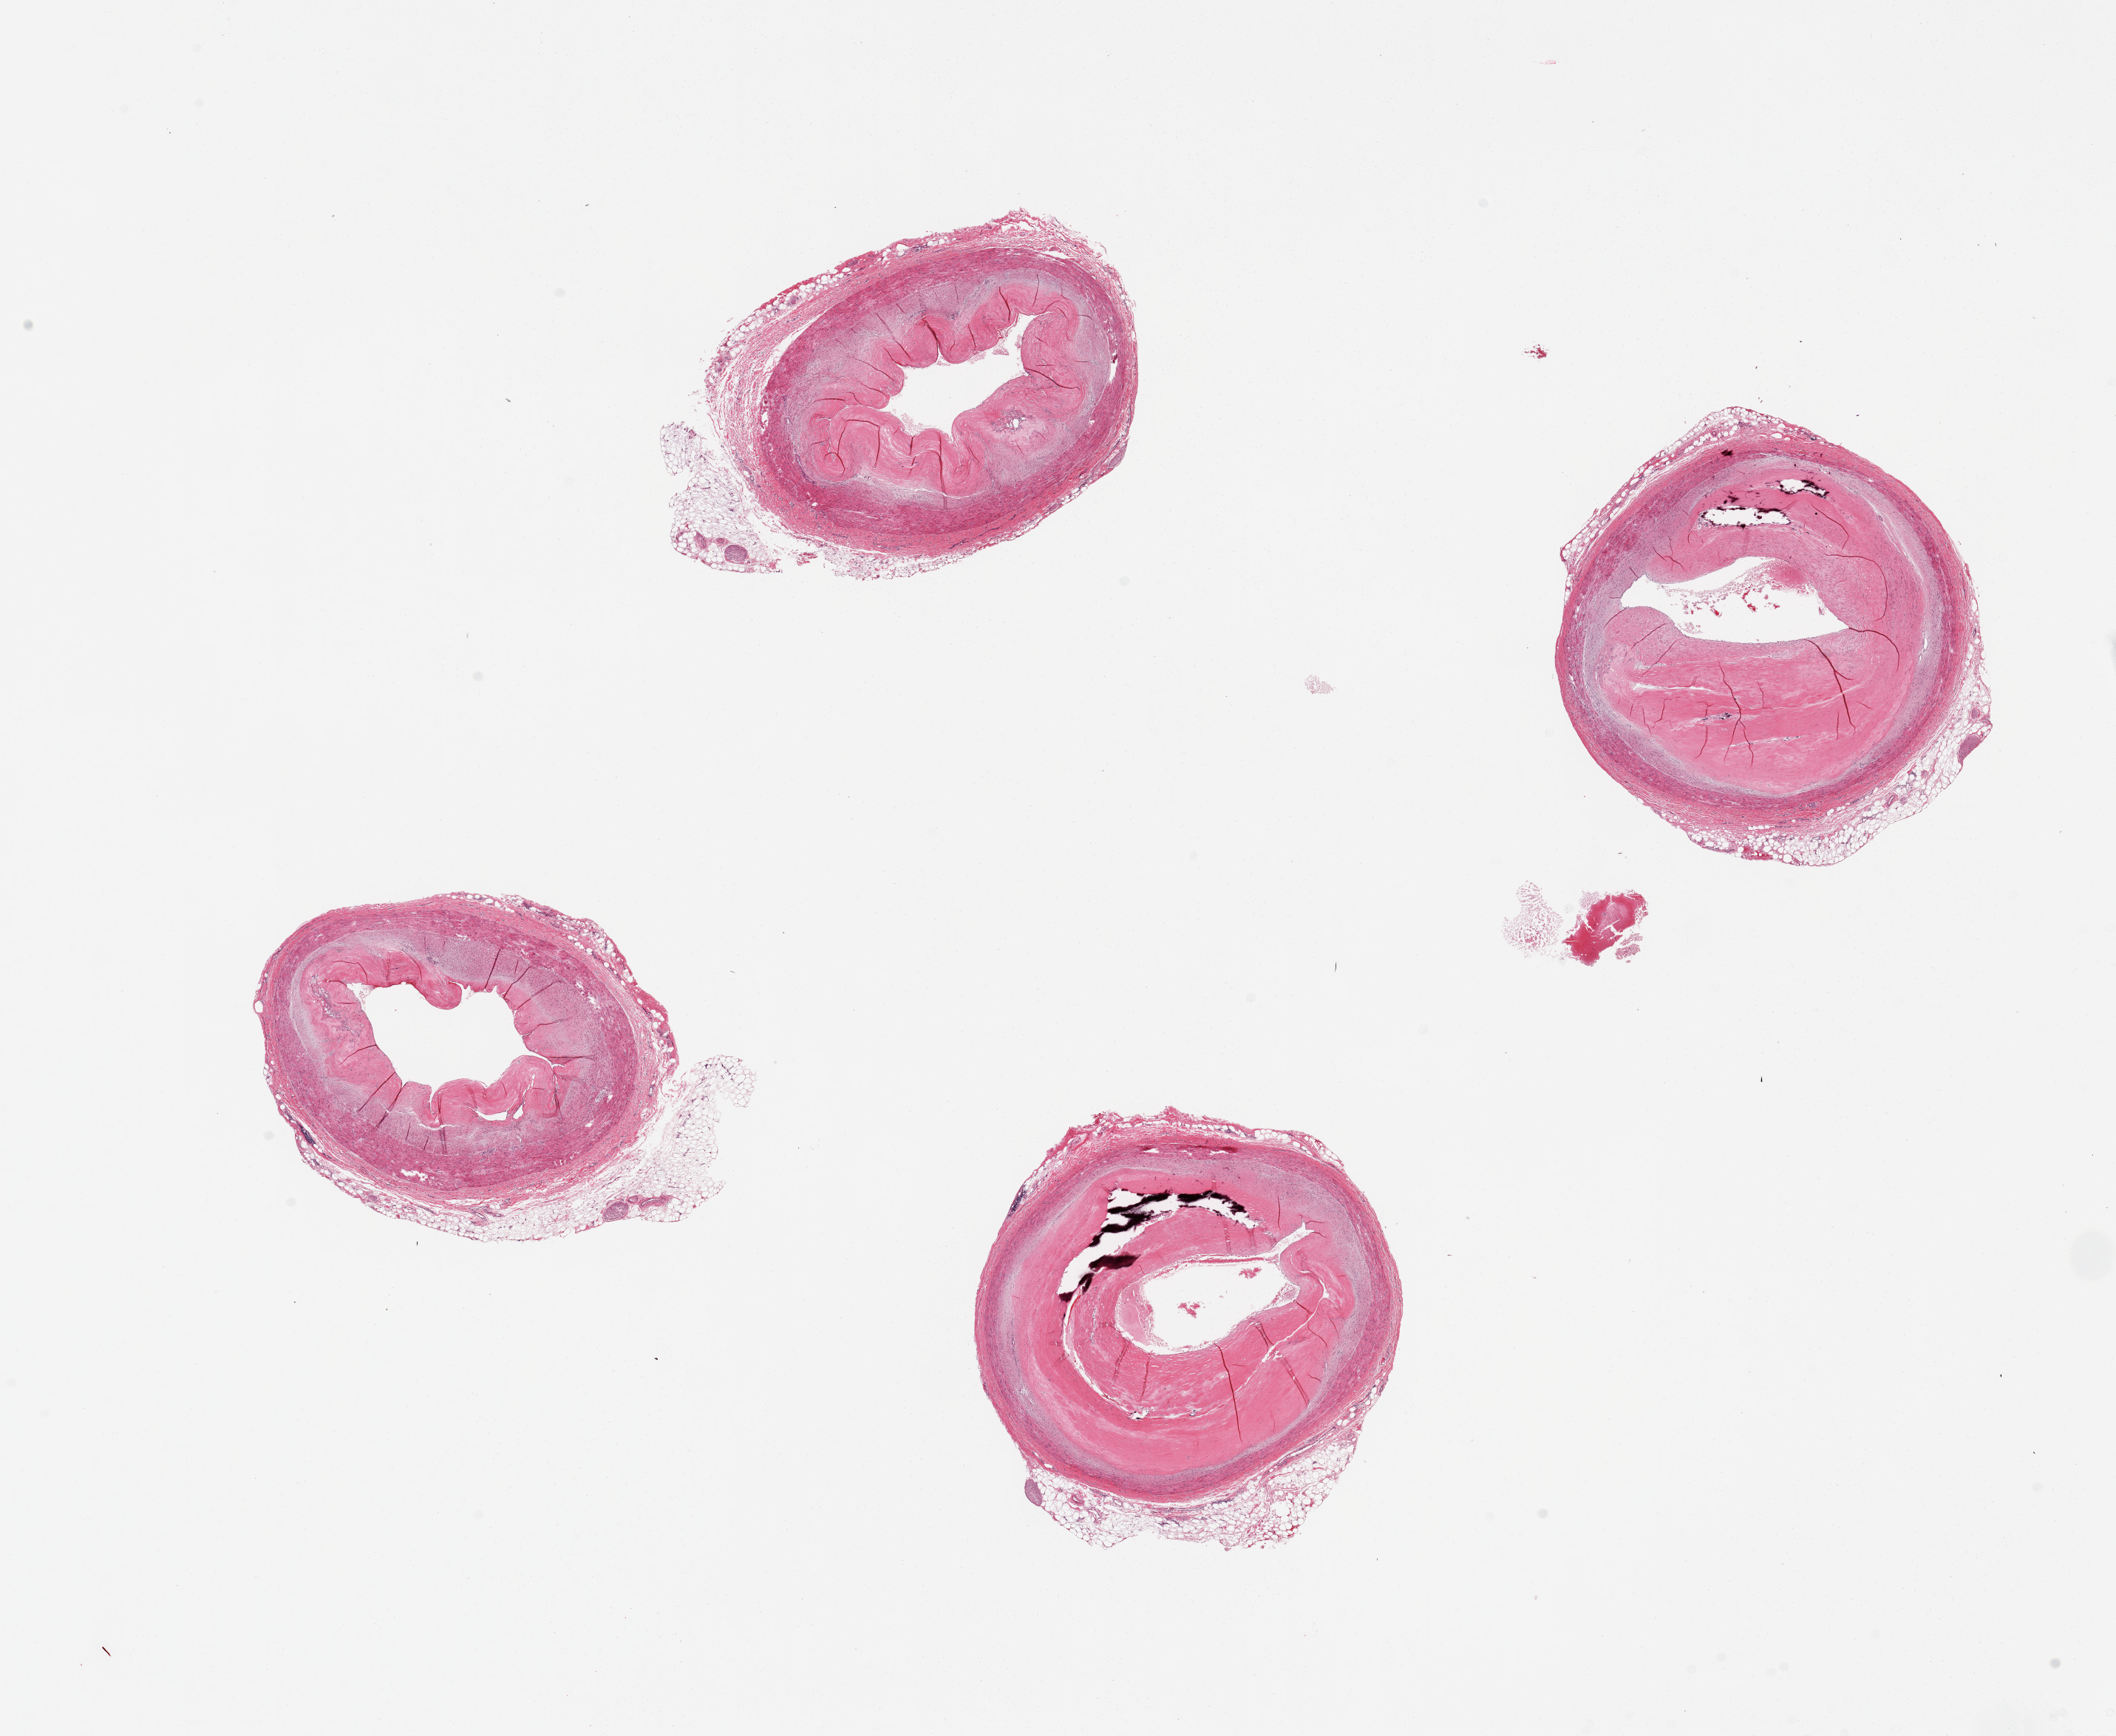
Digitized hematoxylin and eosin (H&E)-stained section — low-resolution overview of the scanned area, about 22.6 x 18.6 mm. PAXgene-fixed, paraffin-embedded tissue. Section of coronary artery (target tissue). Tissue donor sample. Male donor.
- reviewer comment on this tissue sample: 4 pieces, each ~5x4mm; sclerotic plaque and medial calcification